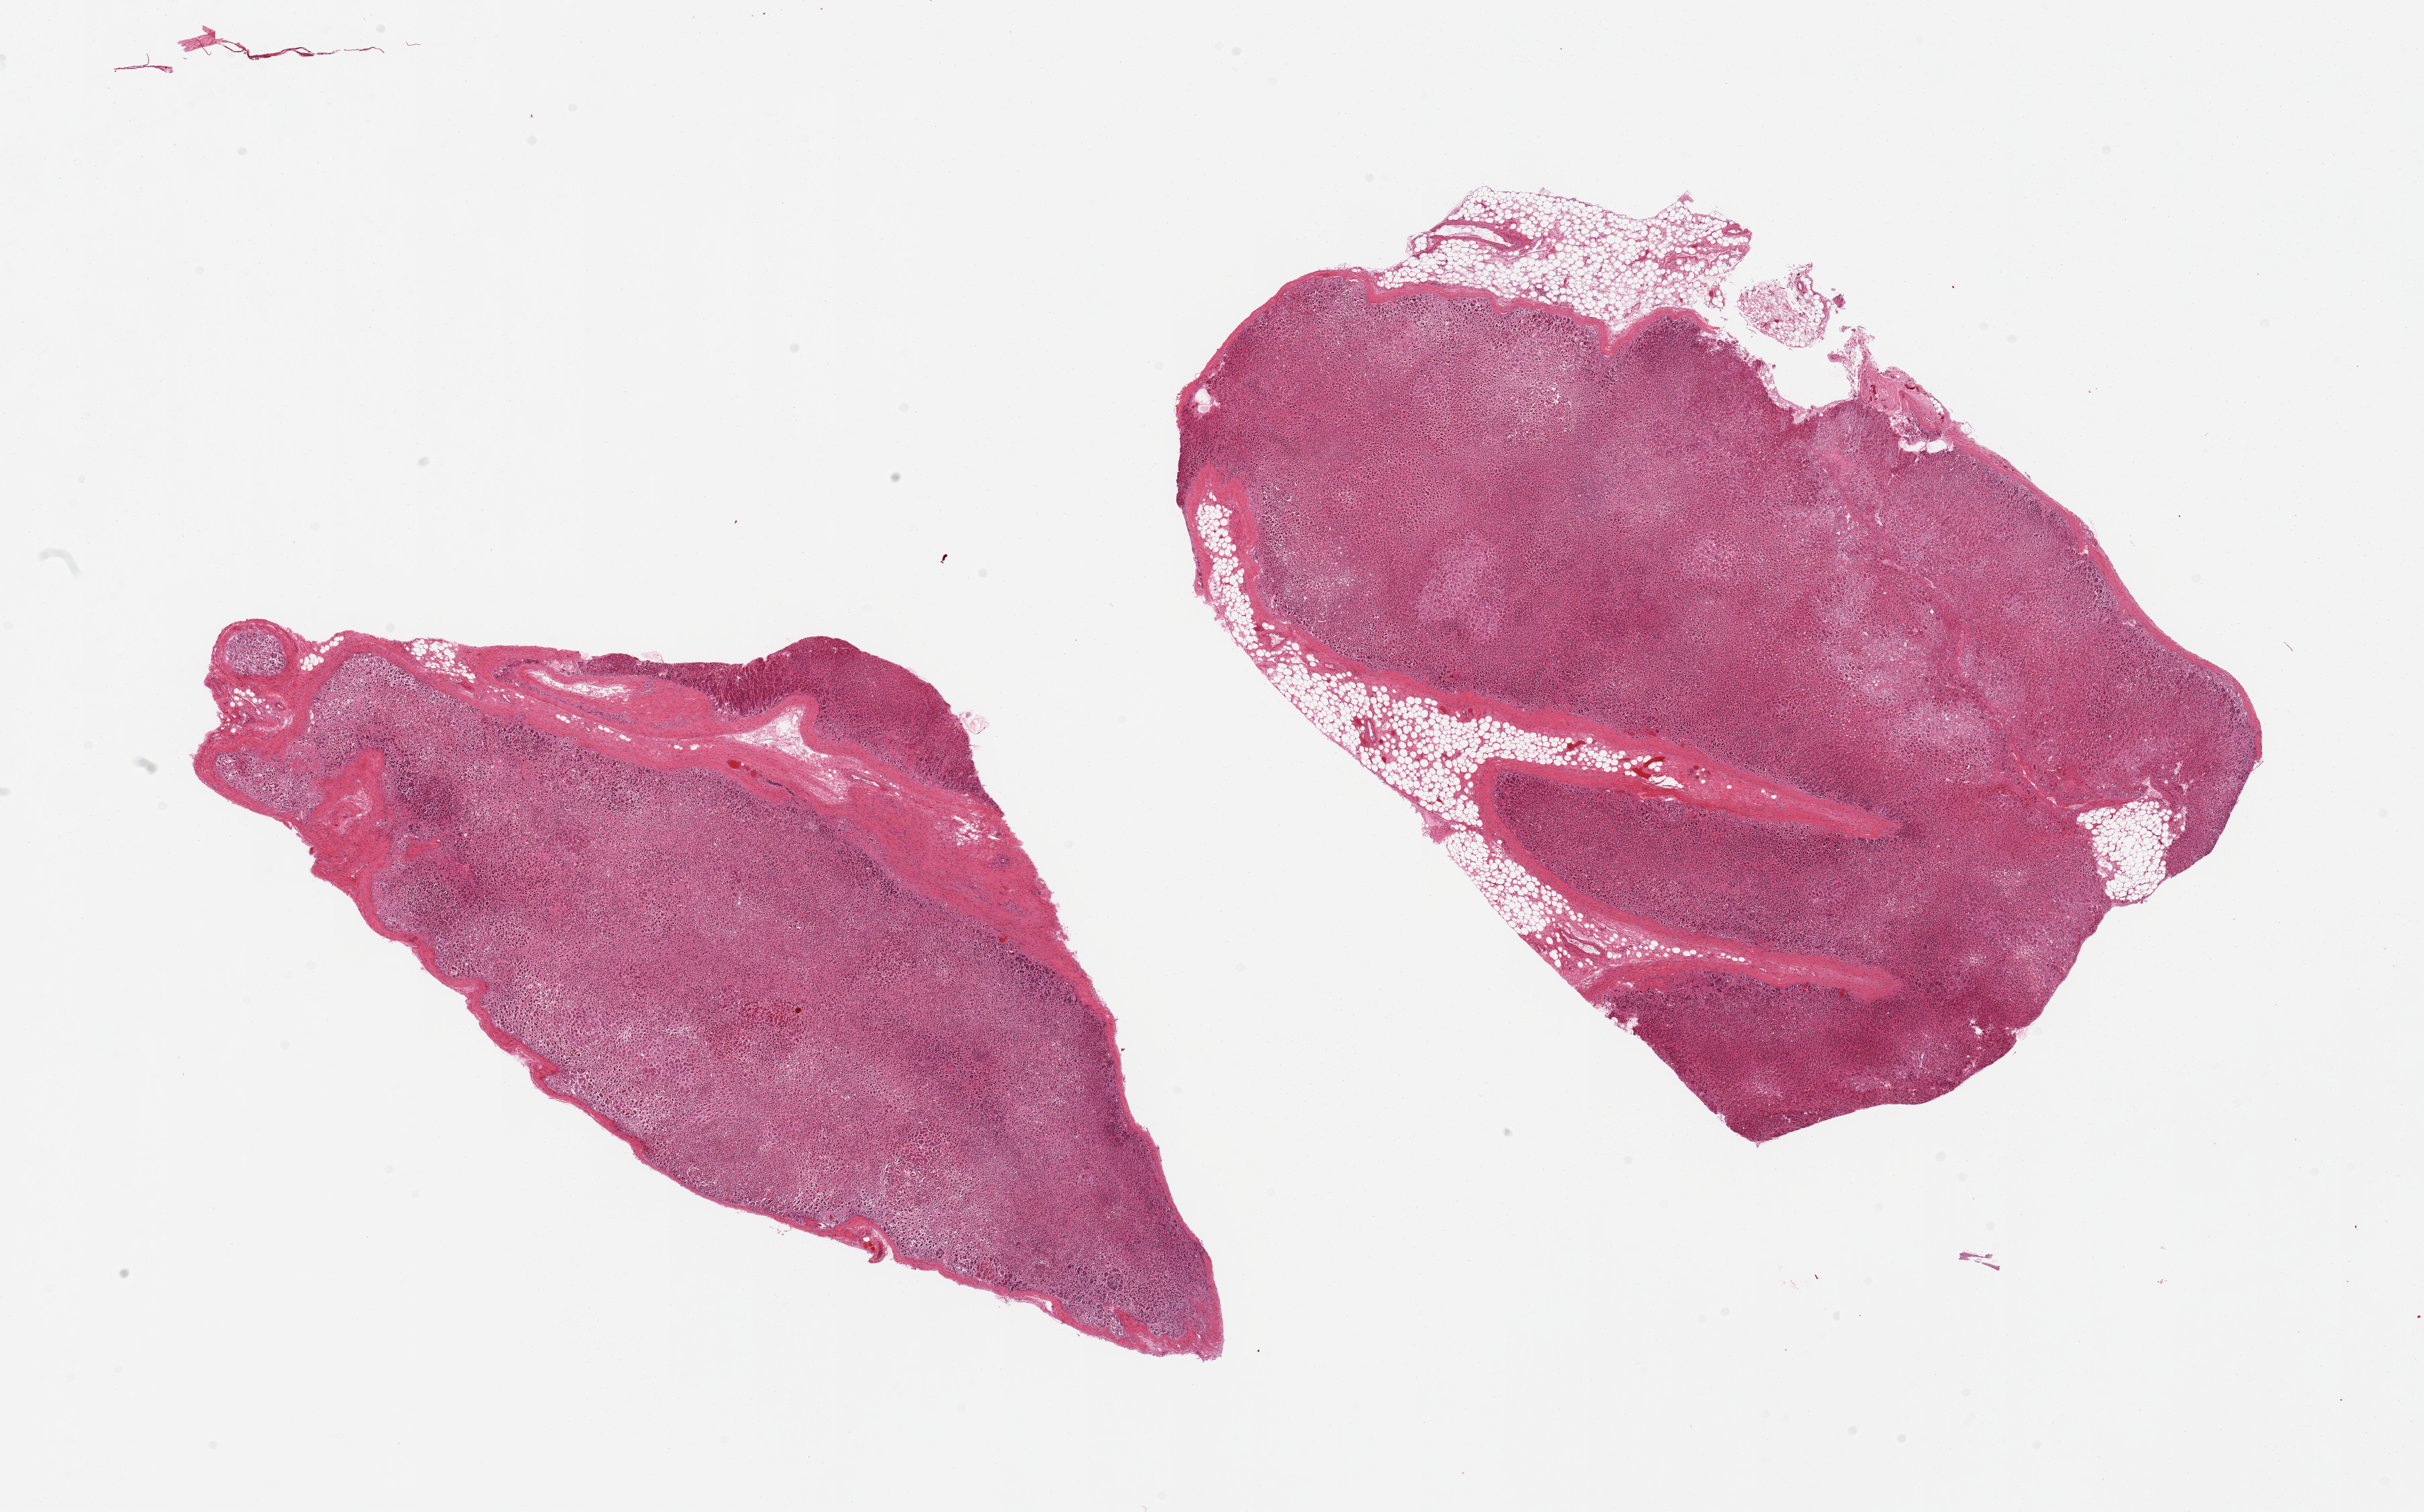
Whole-slide image, hematoxylin and eosin (H&E) stain, brightfield, low-resolution overview of the scanned area, about 28.5 x 17.8 mm, PAXgene-fixed, paraffin-embedded tissue, section of adrenal gland (target tissue), donor tissue sample.
Pathologist's review note for this sample: 6 pieces, all cortex, markedly autolyzed, ~10% adherent fat.